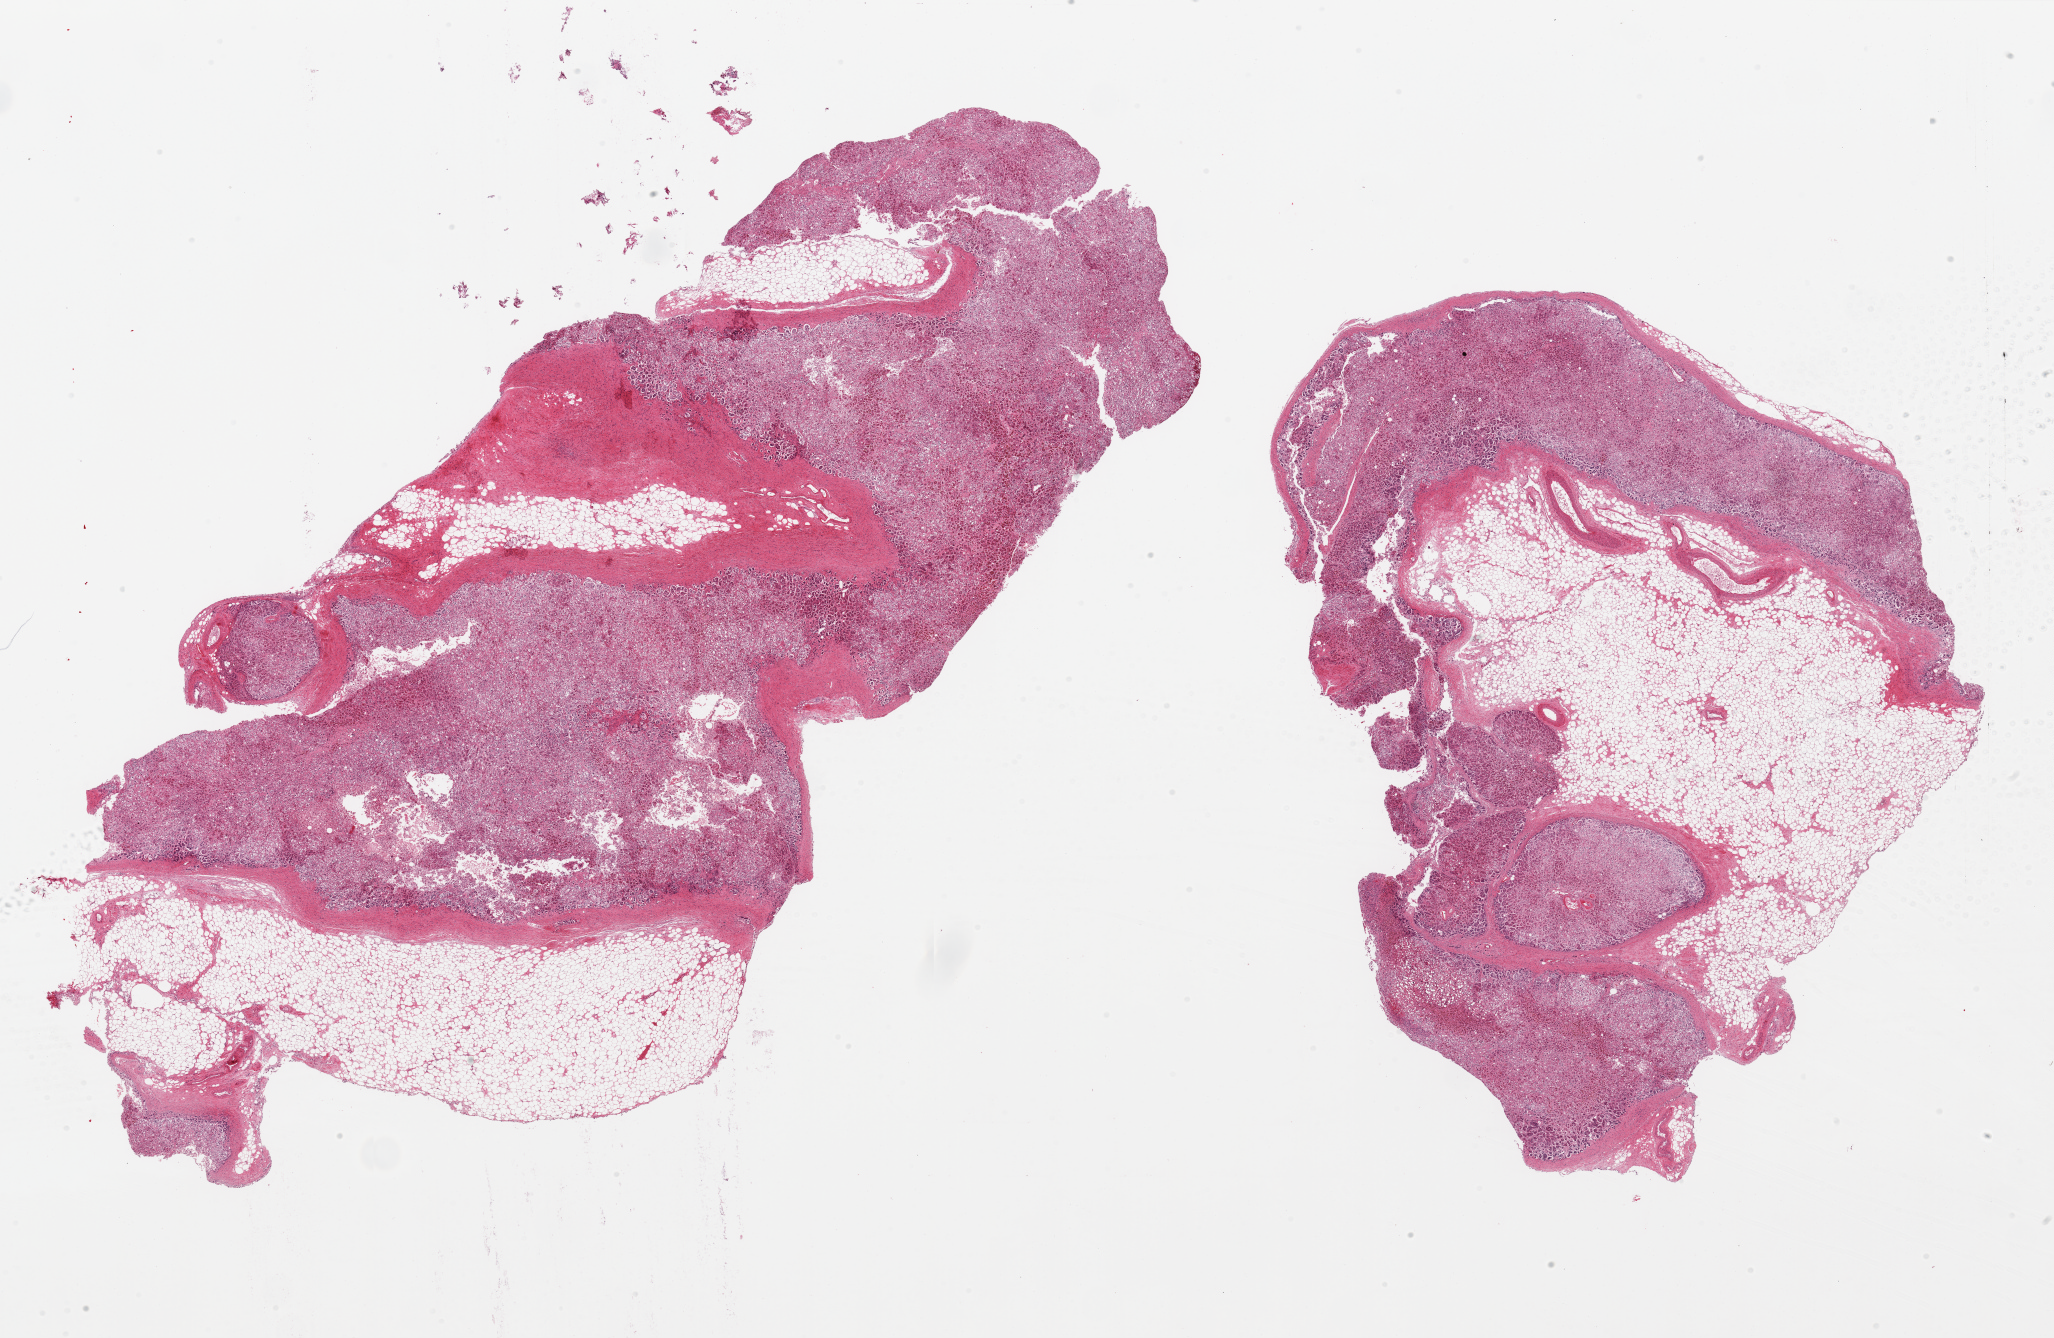
Digitized H&E-stained section, brightfield — shown as a low-resolution overview of the whole scanned area (about 32.5 x 21.2 mm, from a 20x scan). PAXgene-fixed paraffin-embedded (PFPE) section. Target tissue: adrenal gland. Donor tissue sample. Male donor.
* review note (as recorded): 2 pieces, ~40% adherent/intersitial fat; All cortex, moderately advanced autolysis